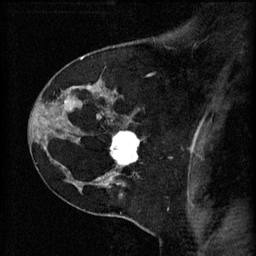
Breast MRI (dynamic contrast-enhanced), one sagittal slice. Slice 43 of 60 in the series (ordered by position). 3 images stored at this slice position (order not interpretable as contrast timing). 1.5 T. TE 4.2 ms, TR 11 ms. 2 mm slice thickness. 256 × 256 image matrix, field of view 180 × 180 mm. Patient: female, 45 years.
Outlined on this slice (semi-automatic segmentation, software-assisted and operator-edited):
- analysis volume of interest (the breast-tissue region the enhancement analysis was run in; not a lesion): bounding box [x1, y1, x2, y2] px = [112, 132, 143, 171]
- tumour enhancement mask (voxels above the 70 % enhancement threshold inside the analysis volume of interest): [112, 132, 141, 165]